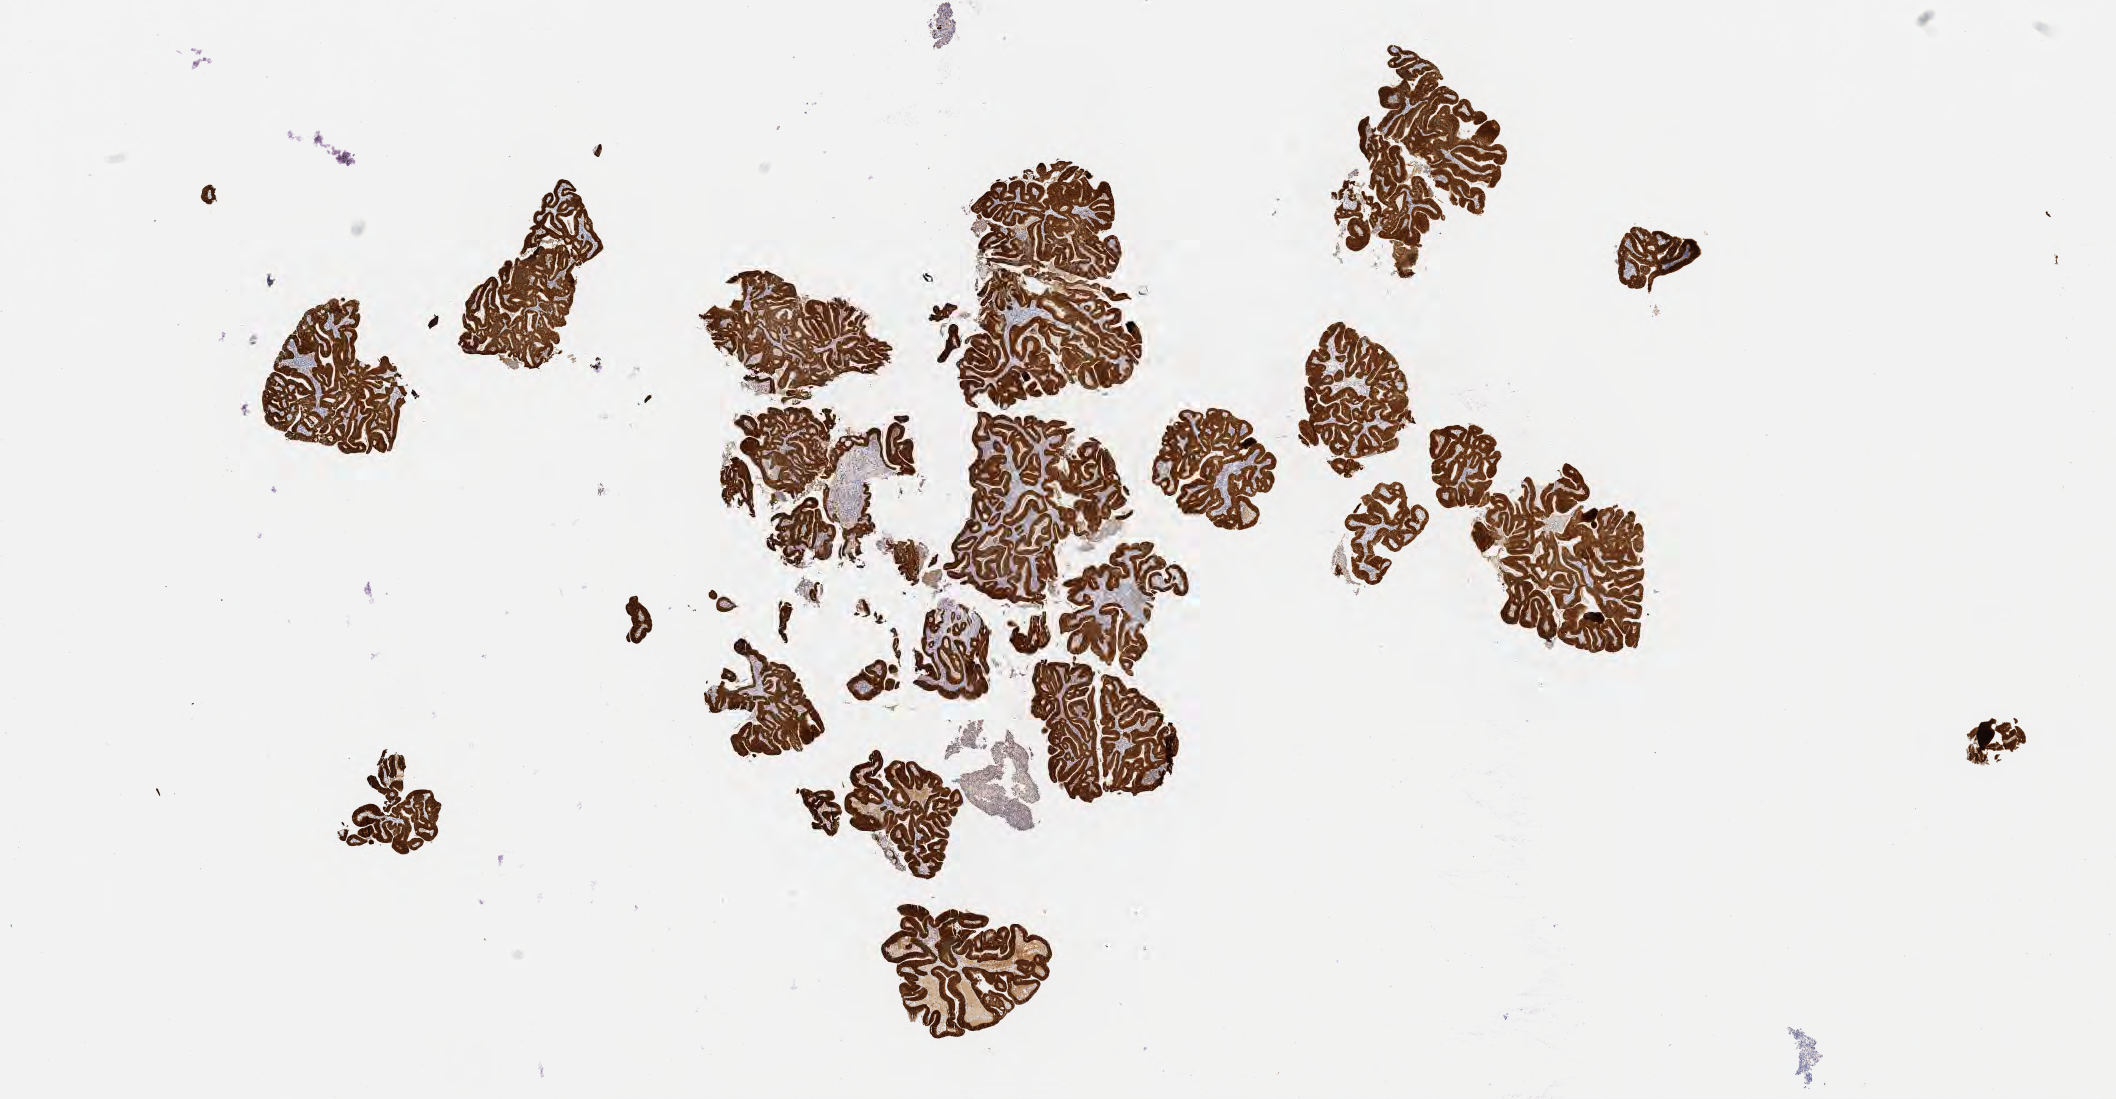
IHC for p16 (p16INK4a), whole-slide image — low-resolution overview of the scanned area, about 17.1 x 8.9 mm, tumor tissue, anatomic site: cervix. Female patient, age 33 years.
• histologic diagnosis: Adenocarcinoma, NOS